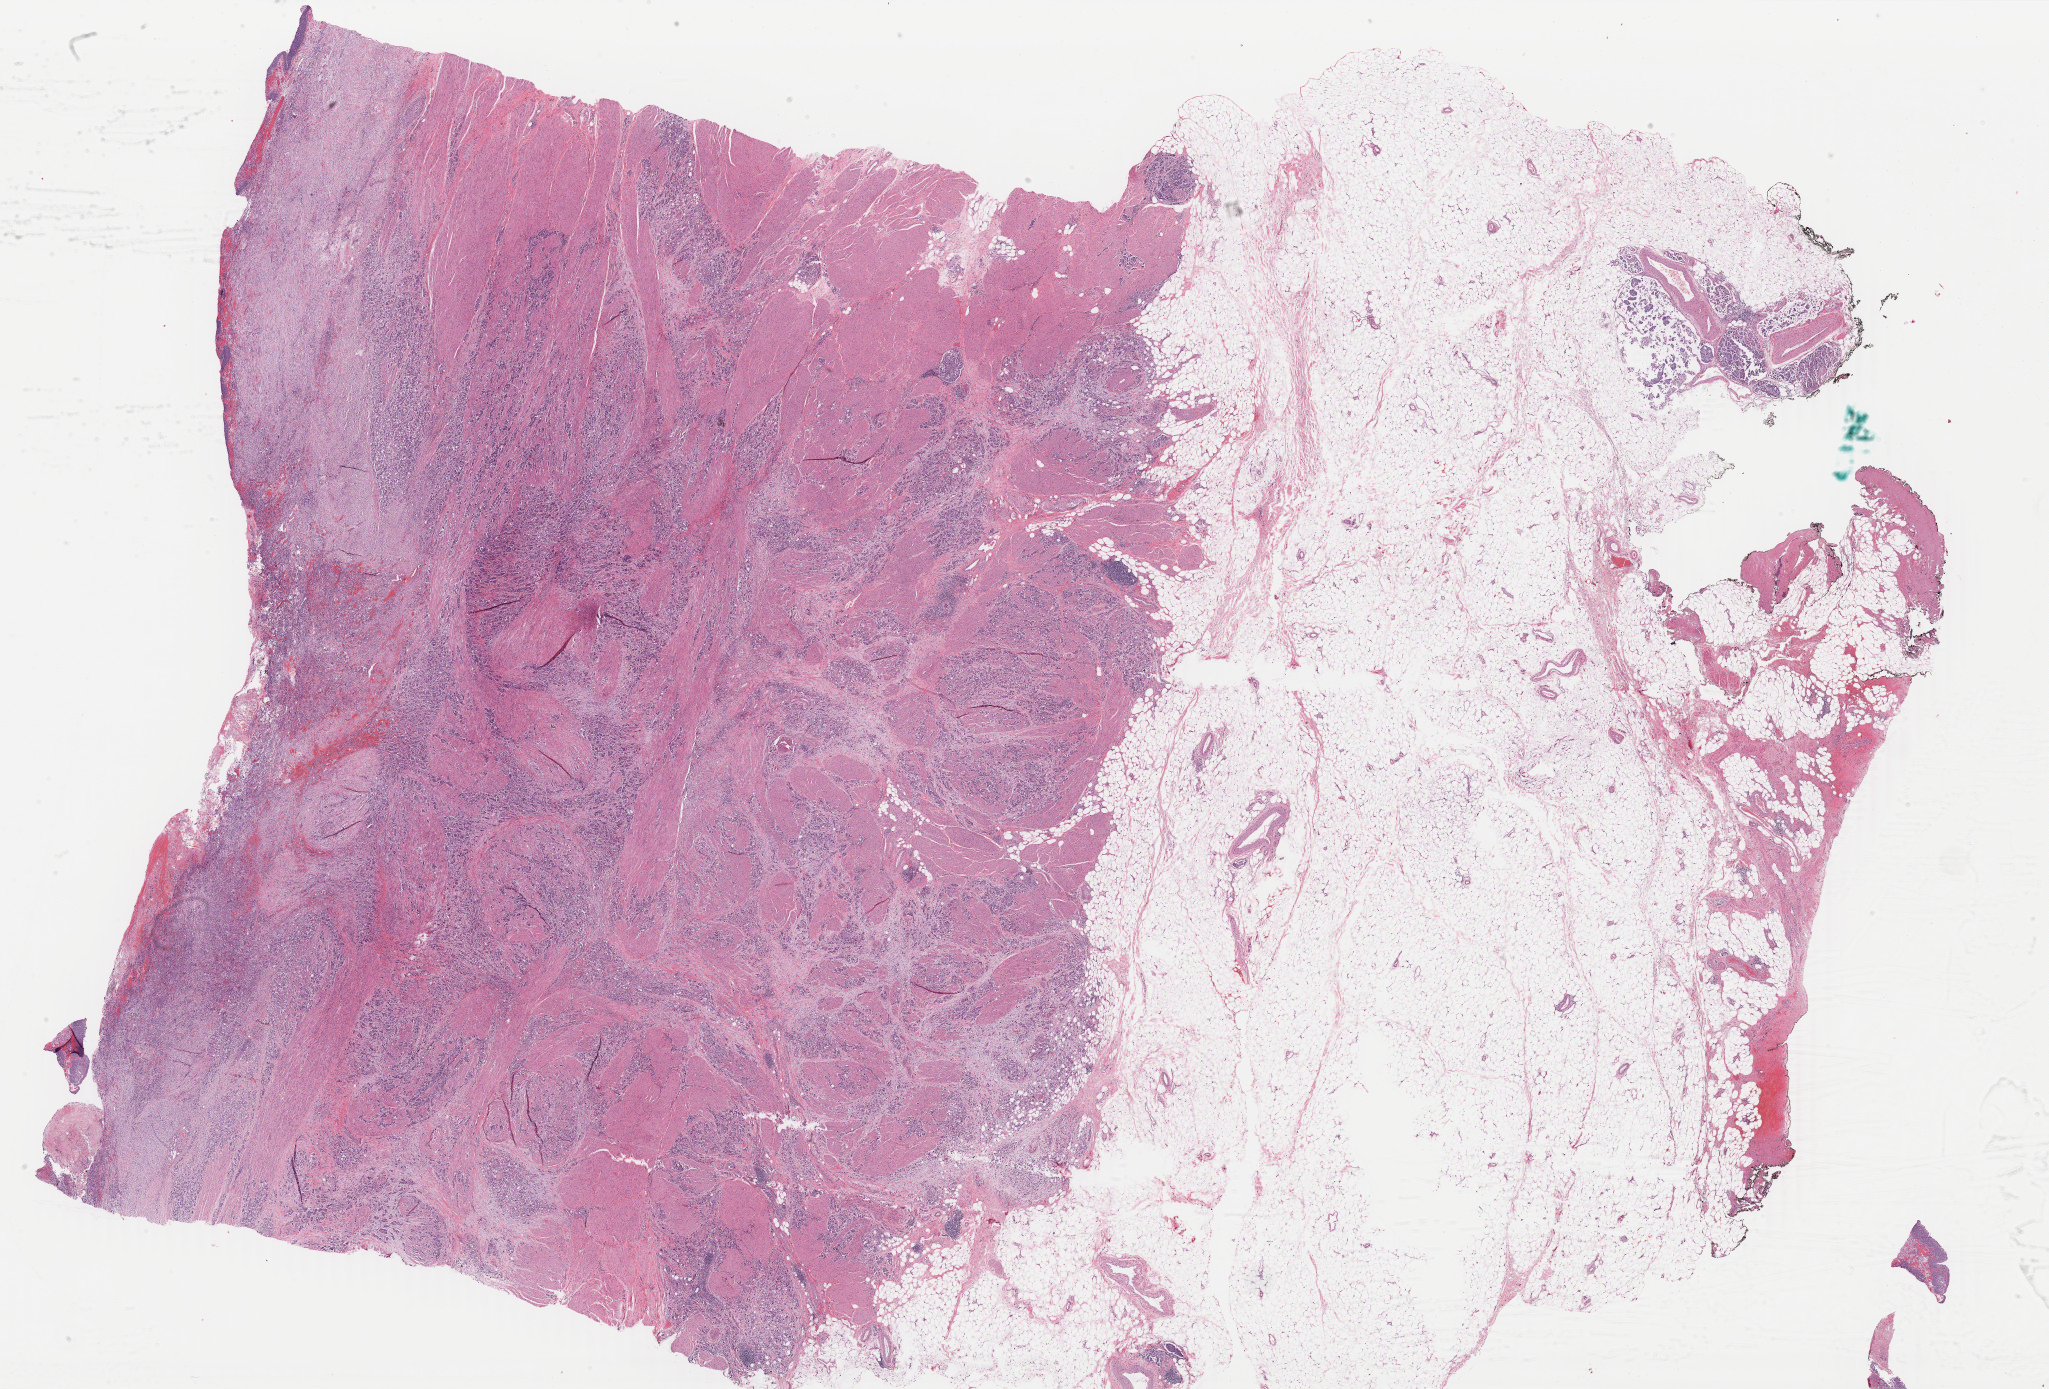
Digitized H&E tissue section (whole slide) — low-resolution overview of the scanned area, about 32.6 x 22.1 mm; FFPE section; sample: primary tumour, bladder. Male, age 60 years at initial diagnosis.
Histologic diagnosis: Transitional cell carcinoma (posterior wall of bladder).